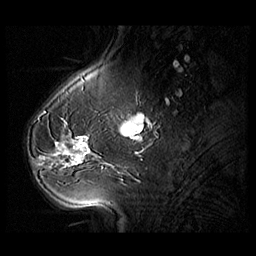
Breast MRI (dynamic contrast-enhanced), one sagittal slice. Position 30 of 104 along the scan axis. 3 images stored at this slice position (order not interpretable as contrast timing). 1.5 T. TE 1.3 ms, TR 5.5 ms. 3 mm slice thickness. 256 × 256 image matrix. Patient: female, 54 years. From the clinical record (not read from this slice): setting: breast cancer imaged before/during neoadjuvant chemotherapy; receptor status: HR-positive, HER2-negative.
Outlined on this slice (semi-automatic segmentation, software-assisted and operator-edited):
- analysis volume of interest (the breast-tissue region the enhancement analysis was run in; not a lesion): box from (x=28, y=127) to (x=104, y=182) px
- tumour enhancement mask (voxels above the 140 % enhancement threshold inside the analysis volume of interest): (x=41, y=136)–(x=89, y=166)